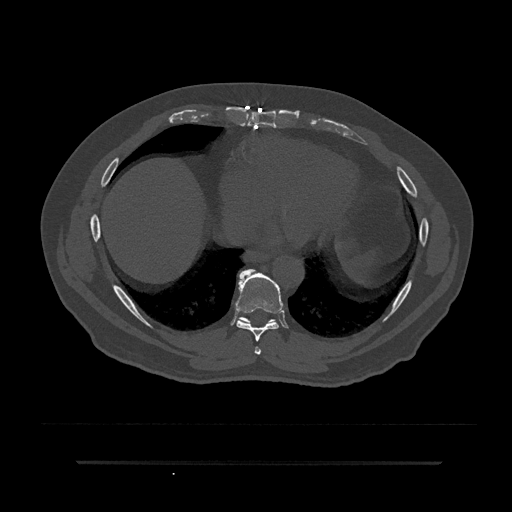
CT including the spine, one axial slice; slice 415 of 797 in the series (ordered by position); reconstruction kernel Br40s/3; 120 kVp; bone window (W 1800 / L 400 HU); 512 × 512 image matrix, field of view 464 × 464 mm. Male patient, age 59 years. Case-level facts recorded for this patient, not image findings: primary cancer: bile ducts; vertebrae with lytic lesions (as recorded): T10.
Outlined on this slice (semi-automatically segmented with operator editing):
- T7 vertebra: bounding box <254,346,261,355> (left, top, right, bottom; pixels)
- T8 vertebra: <235,269,283,342>
- T9 vertebra: <238,317,275,323>